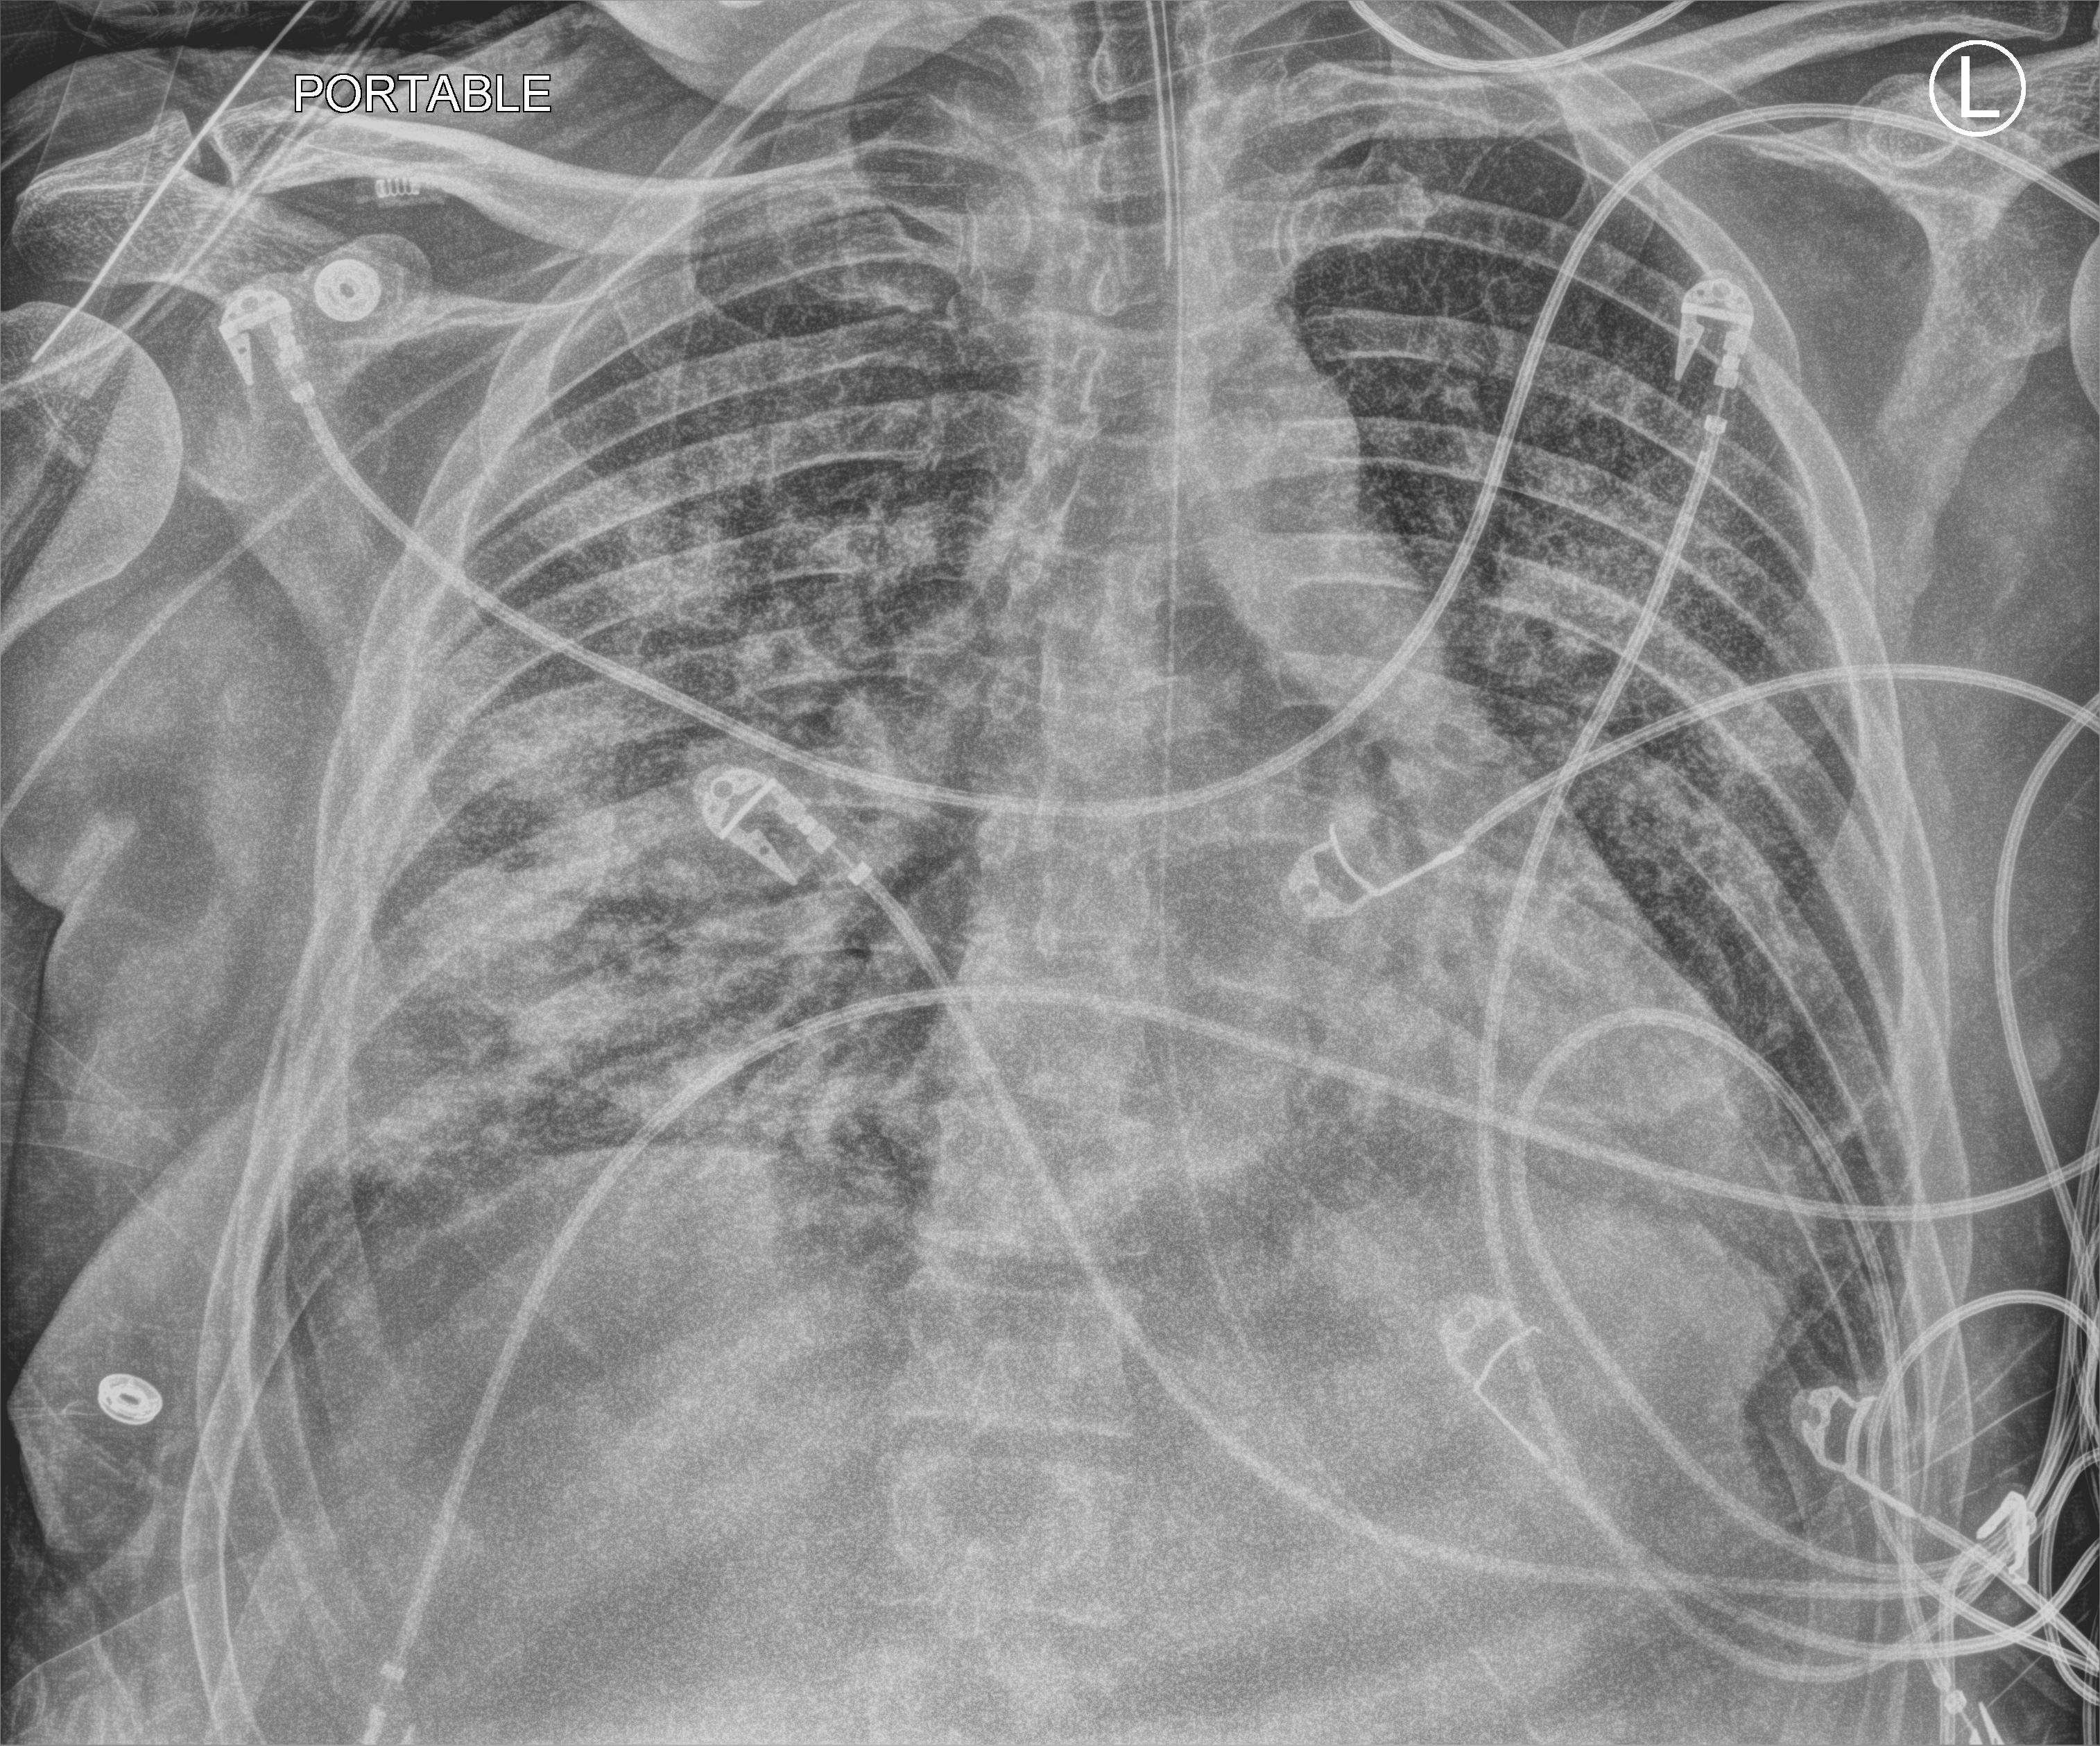
Chest X-ray (portable). Male patient hospitalised with COVID-19, age 18–59 years.
Hospital-stay facts (about this admission, not read from this image; timing relative to this image not recorded):
- admitted to intensive care during this hospital stay: yes
- mechanically ventilated during this hospital stay: yes
- smoking status (admission record): never